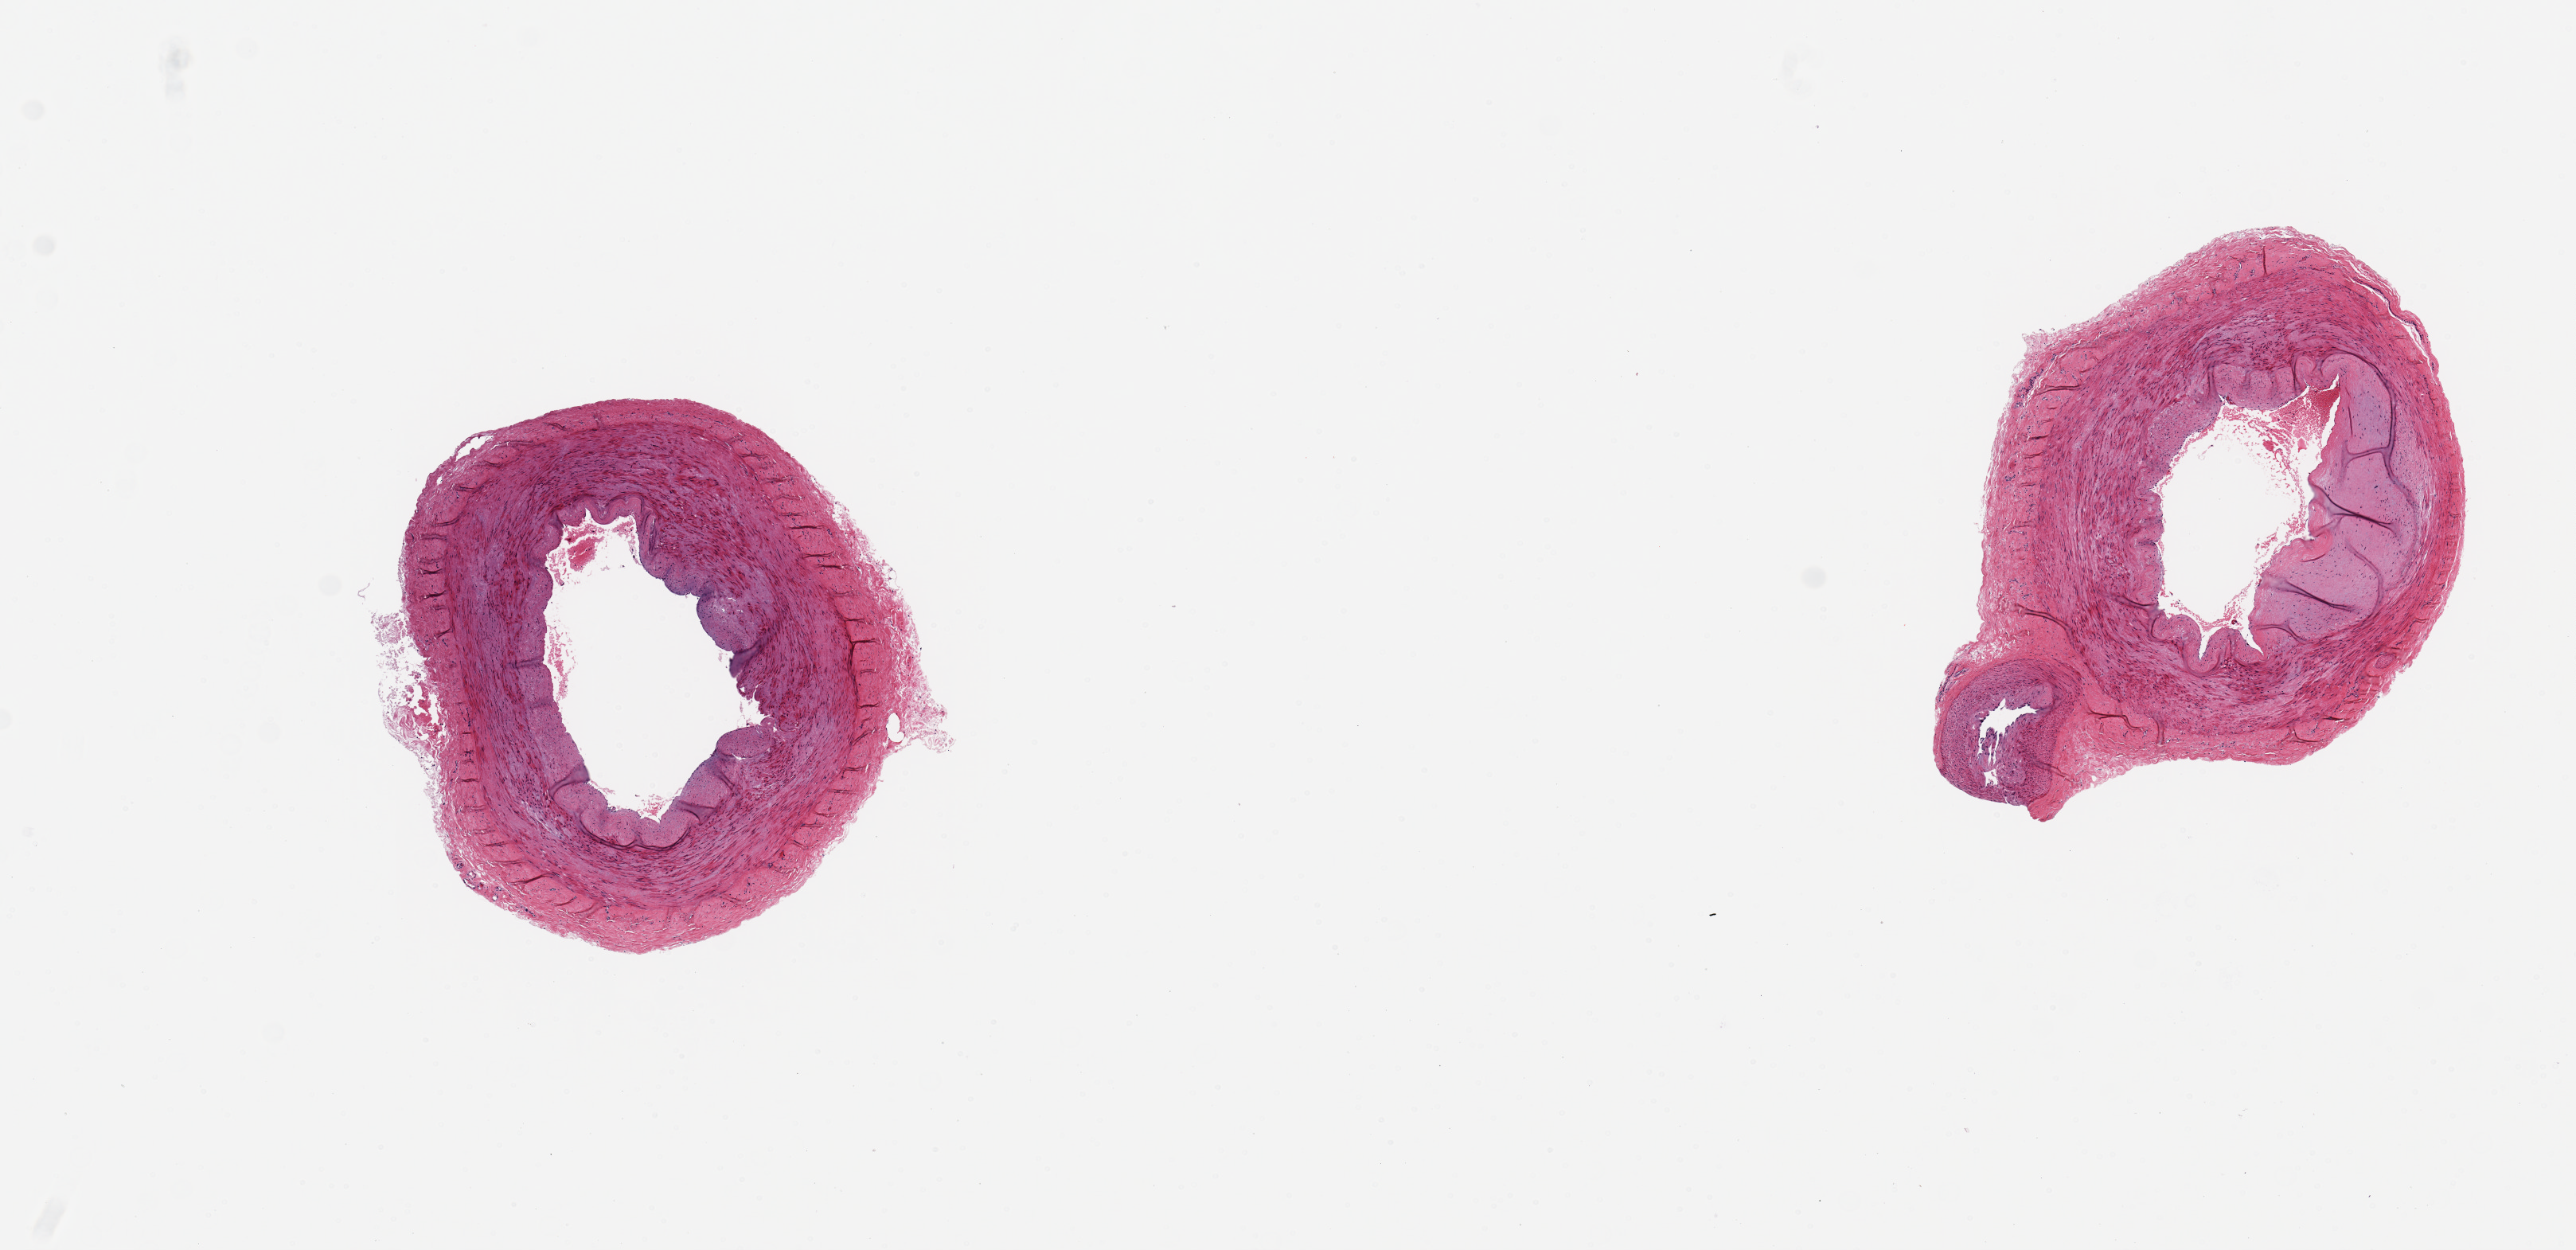
Whole-slide image, hematoxylin and eosin (H&E) stain, a low-resolution overview of the entire scanned area, about 12.8 x 6.2 mm, PAXgene-fixed, paraffin-embedded tissue, section of tibial artery (target tissue), donor tissue sample. Donor sex: male.
Pathologist's review note for this sample: 2 pieces unusually badly autolyzed.